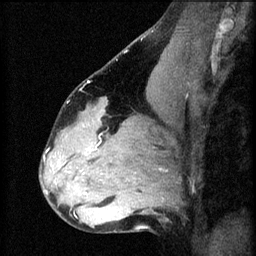
Breast MRI (dynamic contrast-enhanced), one sagittal slice; 3 images stored at this slice position (order not interpretable as contrast timing); 1.5 T; TE 4.2 ms, TR 8.2 ms; 256 × 256 image matrix. Patient: female, 37 years.
Outlined on this slice (semi-automatic segmentation, software-assisted and operator-edited):
- analysis volume of interest (the breast-tissue region the enhancement analysis was run in; not a lesion): bounding box (x1, y1, x2, y2) in pixels: (67, 120, 122, 179)
- tumour enhancement mask (voxels above the 70 % enhancement threshold inside the analysis volume of interest): (95, 138, 101, 151)